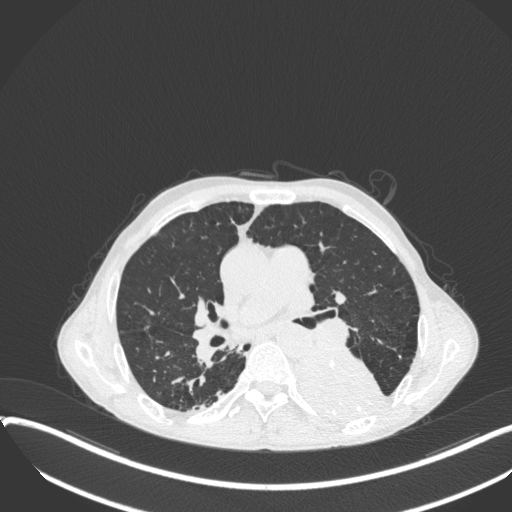
Chest CT, one axial slice; slice 212 of 400 in the series (ordered by position); 120 kVp; lung window (W 1500 / L -600 HU); 1 mm slice thickness; 512 × 512 image matrix, field of view 400 × 400 mm. Patient: male, 57 years. From the clinical record (not read from this slice): clinical TNM (as recorded): T4 N0 M0.
Structures marked on this image (rectangle marked by the reading radiologist):
- lung tumour (recorded histology: squamous cell carcinoma): bounding box (x1, y1, x2, y2) in pixels: (292, 346, 384, 426)